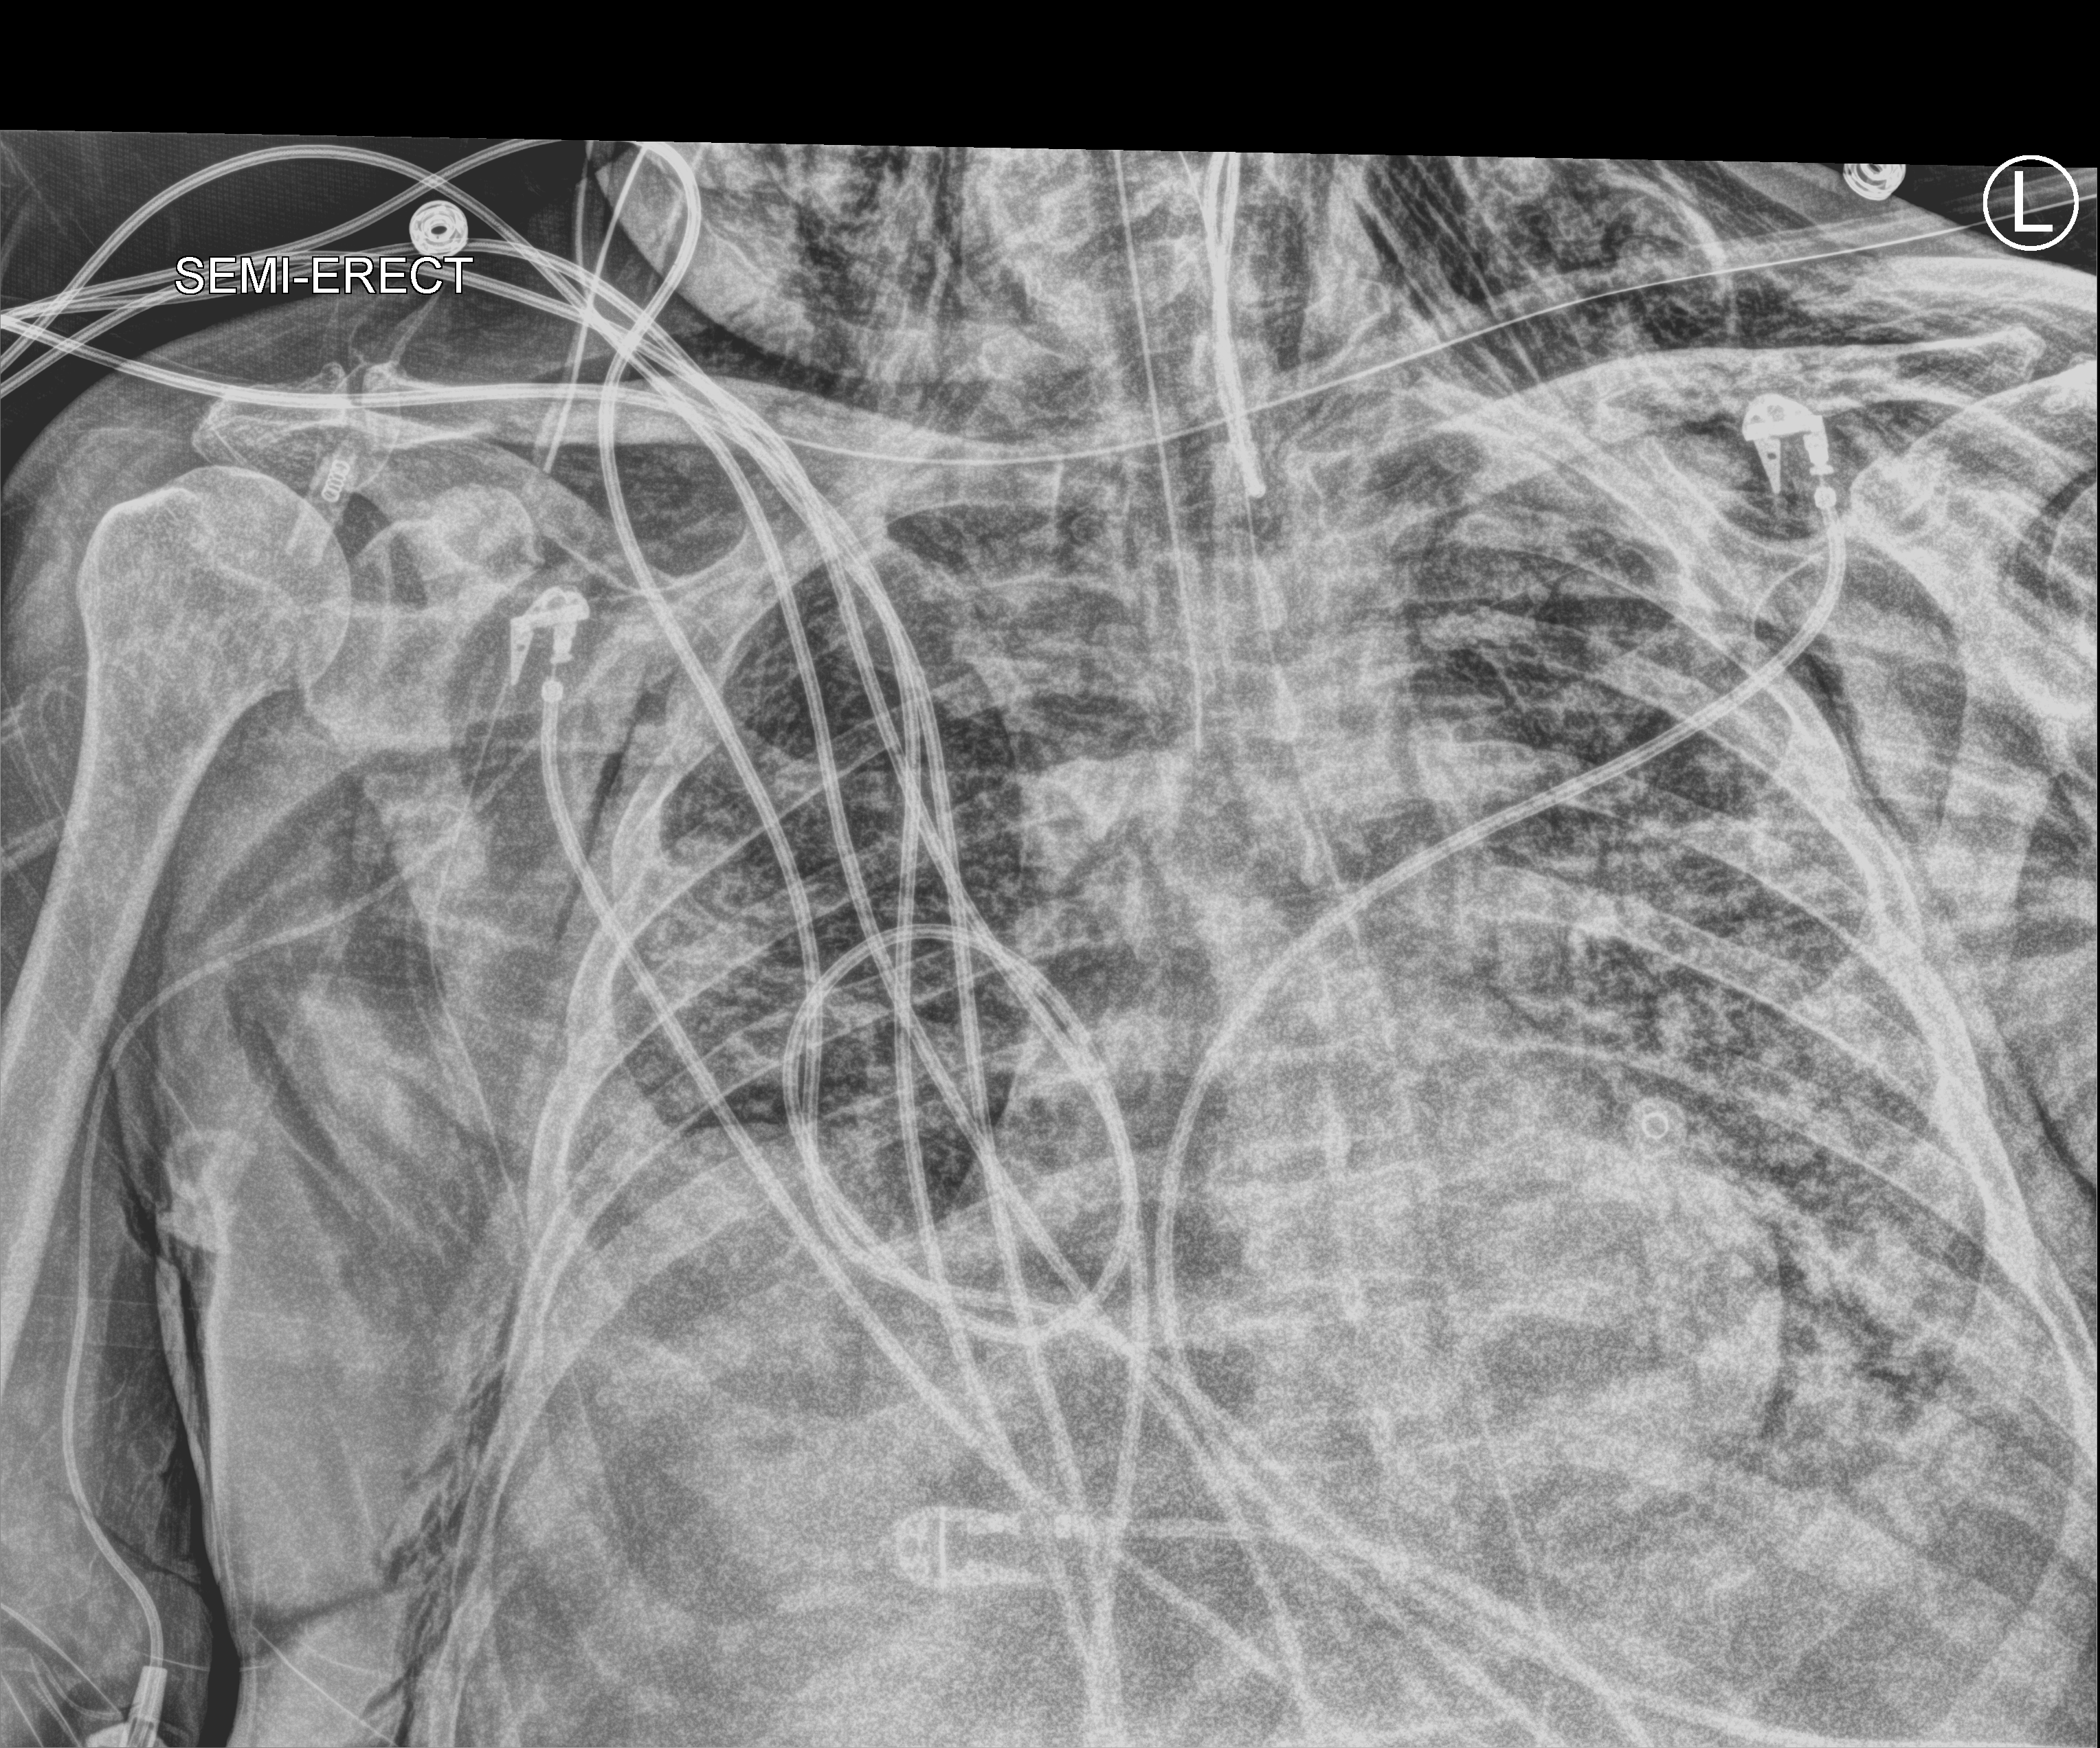
Portable chest radiograph, anteroposterior (AP) projection. Patient hospitalised with COVID-19; male, aged 60–74 years.
Hospital-stay facts (about this admission, not read from this image; timing relative to this image not recorded): diabetes (admission record): yes; admitted to intensive care during this hospital stay: yes.